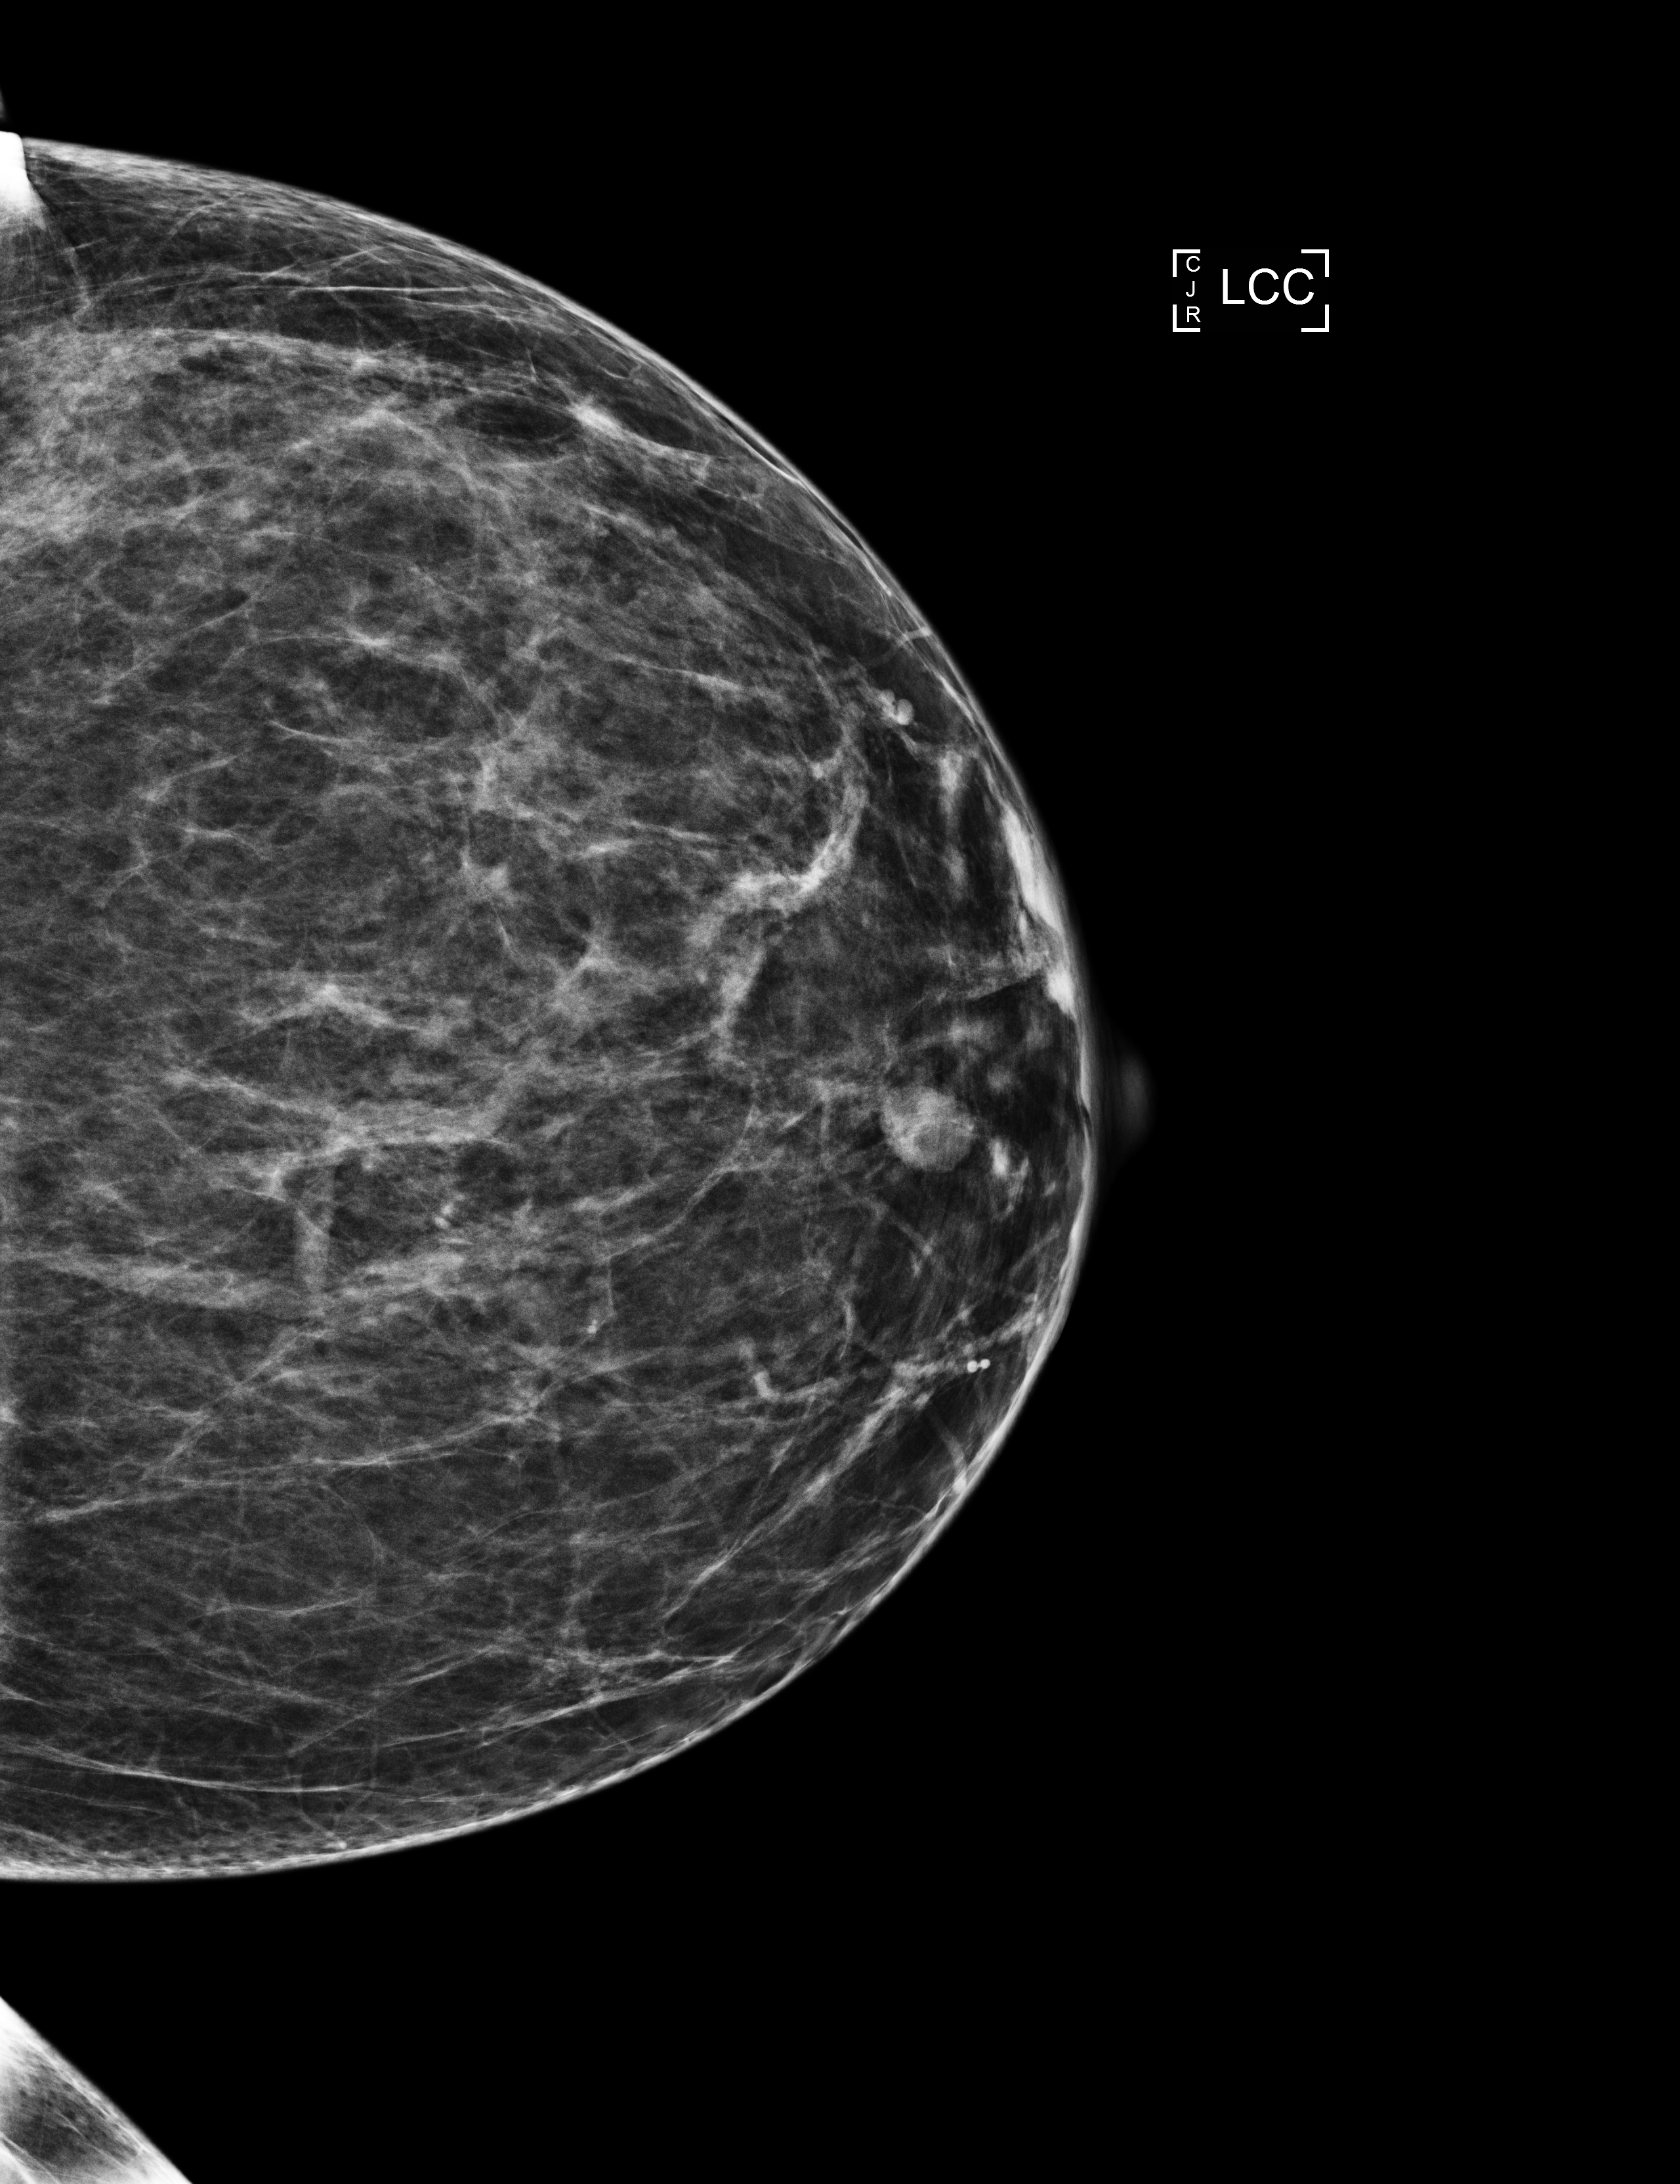
Digital mammogram (FFDM); left breast; cranio-caudal projection; screening examination. Patient: female, 44 years.
BI-RADS breast density category at the screening exam (both breasts, scale 1–4): 3. Final BI-RADS category for the screening round (tomosynthesis exam, both breasts): category 2. Recall: no recall after this screen.